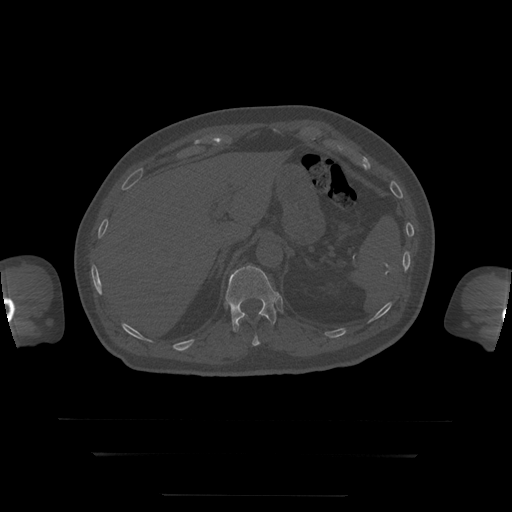
CT including the spine, one axial slice. Slice 83 of 397 in the series (ordered by position). Reconstruction kernel STANDARD. 120 kVp. Bone window (W 1800 / L 400 HU). 1.25 mm slice thickness. 512 × 512 image matrix, field of view 510 × 510 mm. Patient age 73 years. From the clinical record (not read from this slice): primary cancer: prostate.
Annotated regions visible in this slice (semi-automatic segmentation, software-assisted and operator-edited):
- T11 vertebra: box from (x=241, y=317) to (x=276, y=346) px
- T12 vertebra: (x=226, y=266)–(x=280, y=332)